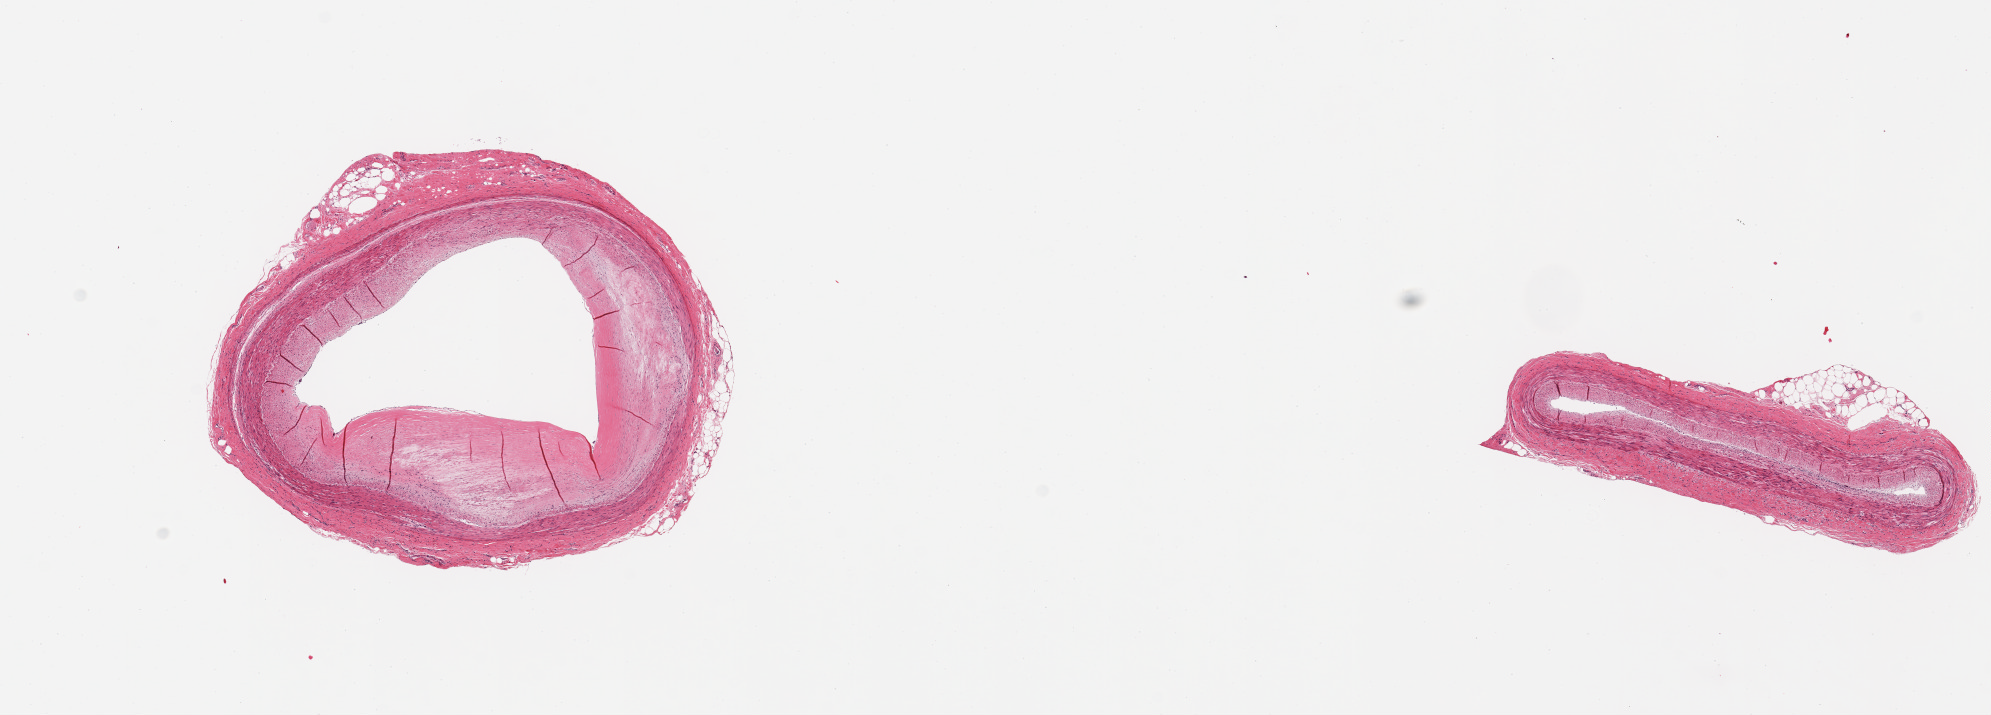
H&E whole-slide image — low-resolution overview of the scanned area, about 15.8 x 5.7 mm (from a 20x scan). PAXgene-fixed, paraffin-embedded tissue. Section of coronary artery (target tissue). Tissue donor sample. Female donor.
* pathologist's review note for this sample: 2 pieces: 1 with large sclerotic plaque, 0.8mm thick; other without plaques